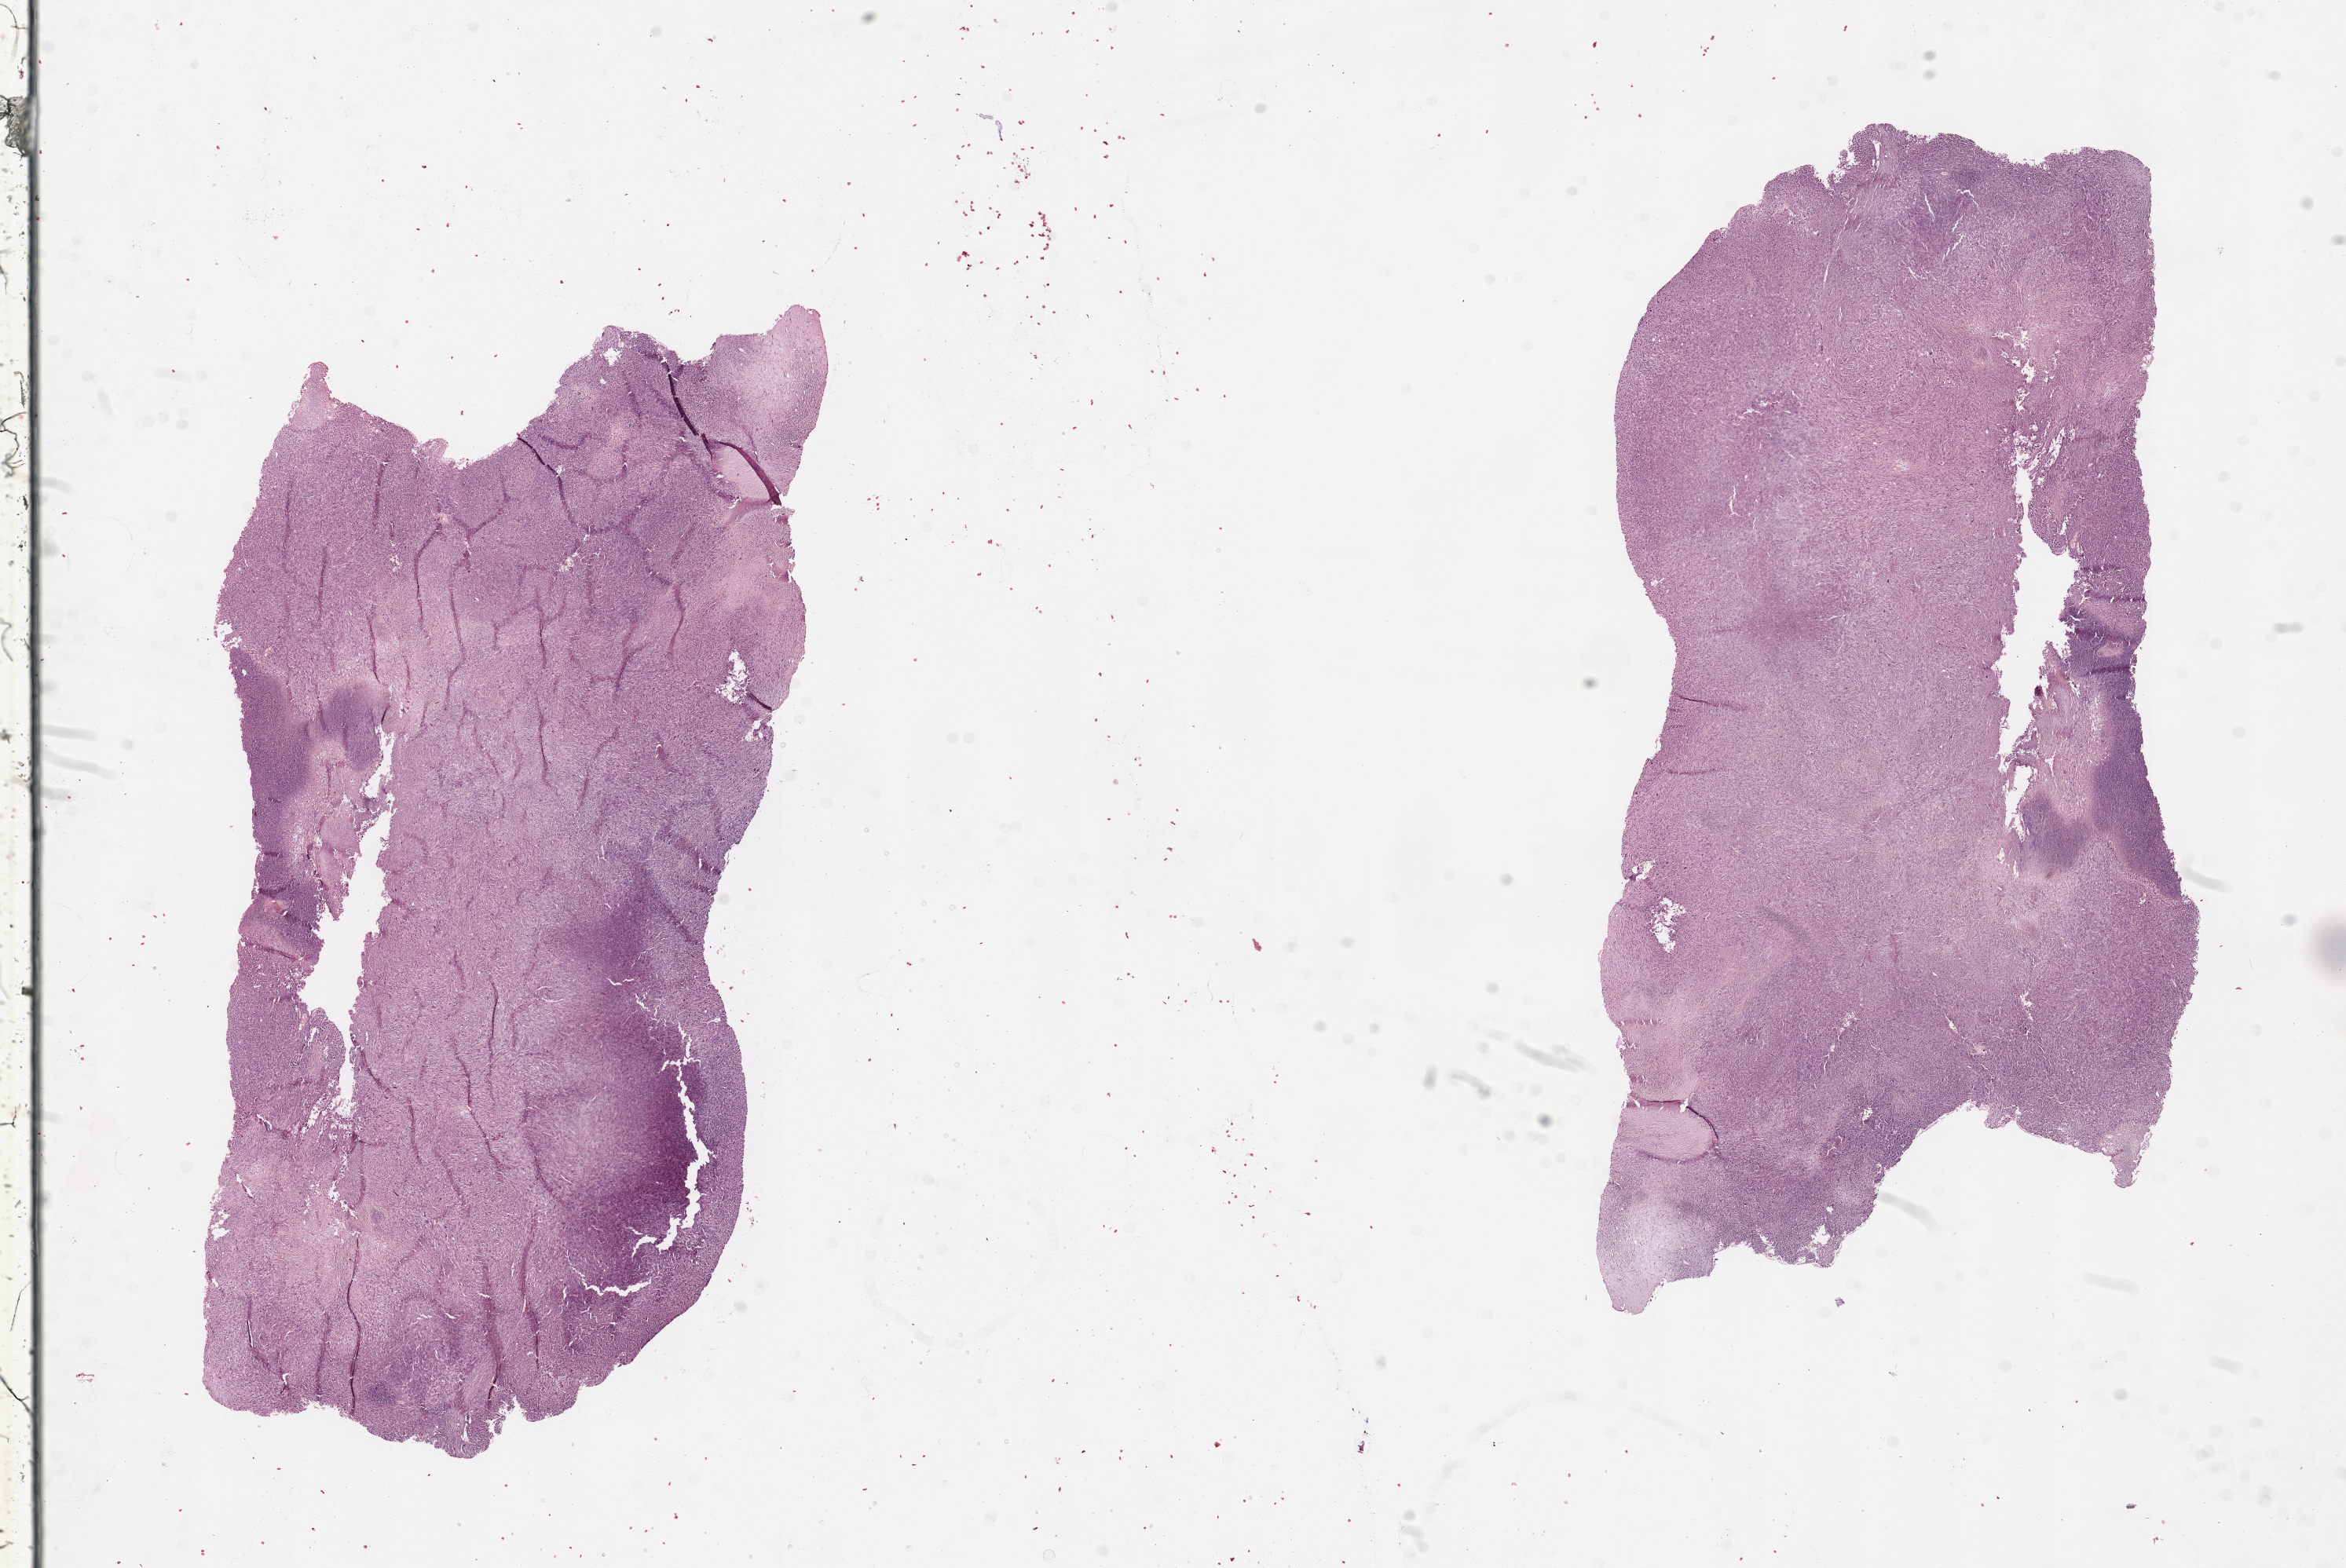
H&E whole-slide image, shown as a low-resolution overview of the whole scanned area (about 23.6 x 15.8 mm); tumour tissue sample. Male, 53 y/o.
Patient diagnosis (cohort enrolment): sarcoma (site not recorded at cohort level).